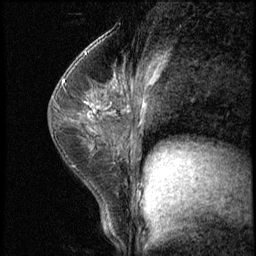
Breast MRI (dynamic contrast-enhanced), one sagittal slice; slice 37 of 62 in the series (ordered by position); 3 images stored at this slice position (order not interpretable as contrast timing); 1.5 T; TE 4.2 ms, TR 8.7 ms; 256 × 256 image matrix, field of view 180 × 180 mm. Patient: female, 35 years. Case-level facts recorded for this patient, not image findings: setting: breast cancer imaged before/during neoadjuvant chemotherapy; receptor status: HER2-positive.
Annotated regions visible in this slice (semi-automatic segmentation, software-assisted and operator-edited):
- analysis volume of interest (the breast-tissue region the enhancement analysis was run in; not a lesion): bounding box (x1, y1, x2, y2) in pixels: (71, 78, 120, 139)
- tumour enhancement mask (voxels above the 140 % enhancement threshold inside the analysis volume of interest): (88, 109, 96, 116)